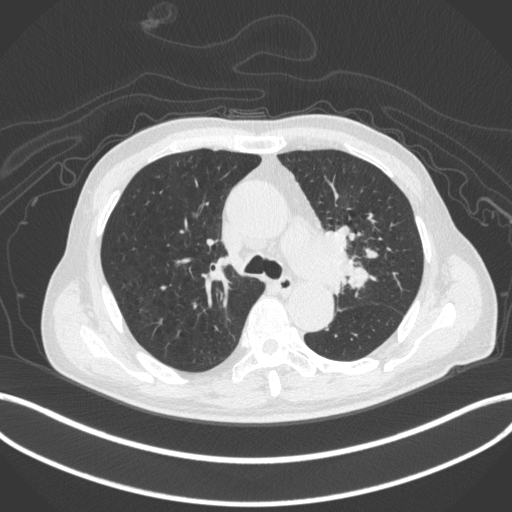
Chest CT, one axial slice; position 289 of 420 along the scan axis; reconstruction kernel B31f; 120 kVp; lung window (W 1500 / L -600 HU); 1 mm slice thickness; 512 × 512 image matrix, field of view 400 × 400 mm. Male patient, age 77 years. From the clinical record (not read from this slice): clinical TNM (as recorded): T3 N1 M0.
Outlined on this slice (rectangle marked by the reading radiologist):
- lung tumour (recorded histology: adenocarcinoma): bounding box <312,224,369,291> (left, top, right, bottom; pixels)